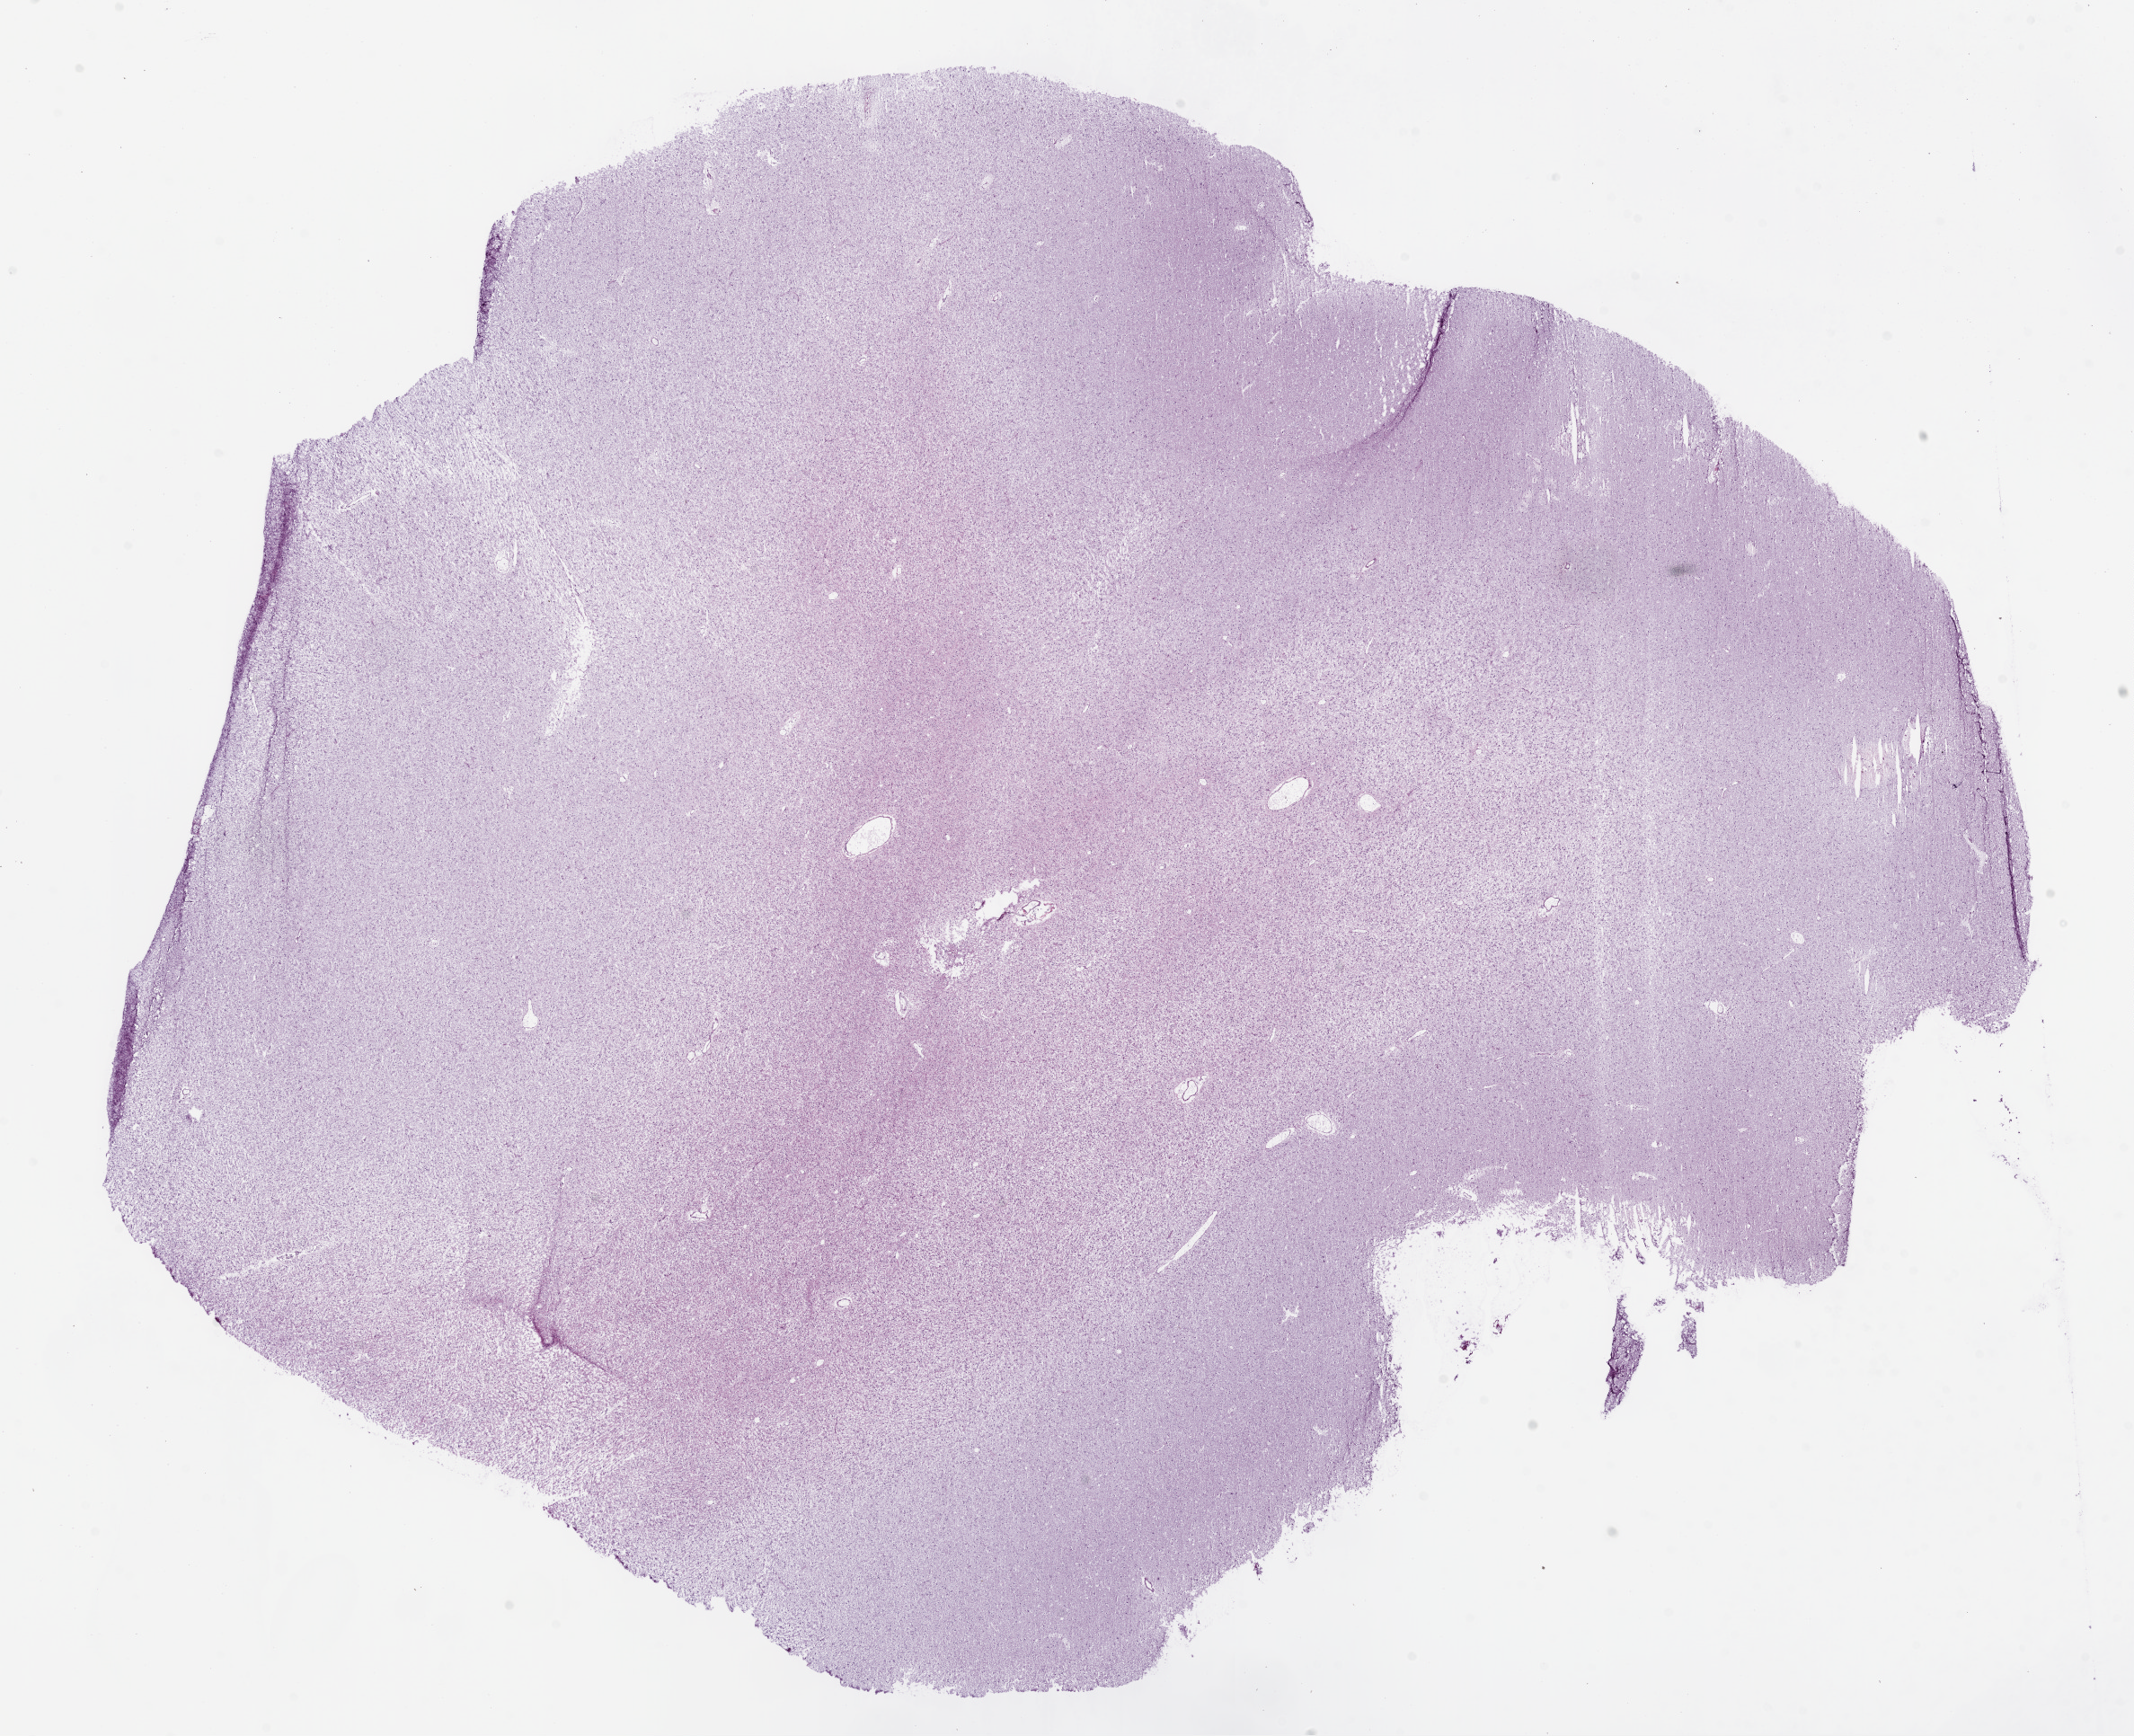
Digitized H&E tissue section (whole slide), a low-resolution overview of the entire scanned area, about 19.1 x 15.5 mm. Frozen section. Sample: primary tumour, brain. Male patient; age at initial diagnosis 17 years. Histologic grade: G2 (moderately differentiated). Composition of this section per pathologist review: tumour cells 100%, tumour nuclei 60%, normal cells 0%, stromal cells 0%, necrosis 0%.
• laterality: left
• histologic diagnosis: Oligodendroglioma, NOS (cerebrum)